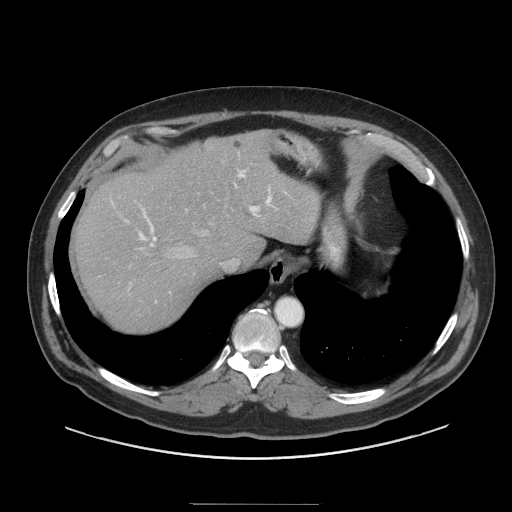
Contrast-enhanced abdominal CT (liver protocol), one axial slice. Position 75 of 91 along the scan axis. Reconstruction kernel STANDARD. 140 kVp. Soft-tissue window (W 400 / L 40 HU). 512 × 512 image matrix. From the clinical record (not read from this slice): diagnosis: hepatocellular carcinoma (patient treated with transarterial chemoembolisation; whether this scan precedes or follows treatment is not stated here); TNM stage (as recorded): Stage-I; Child-Pugh class: A; tumour size: 4 cm.
Annotated regions visible in this slice (semi-automatic segmentation, software-assisted and operator-edited):
- abdominal aorta: bounding box <277,299,302,325> (left, top, right, bottom; pixels)
- liver parenchyma outside the tumour (the mass and vessels are separate outlines, so this box may not span the whole liver): <74,130,320,330>
- liver vessels: <126,153,272,246>